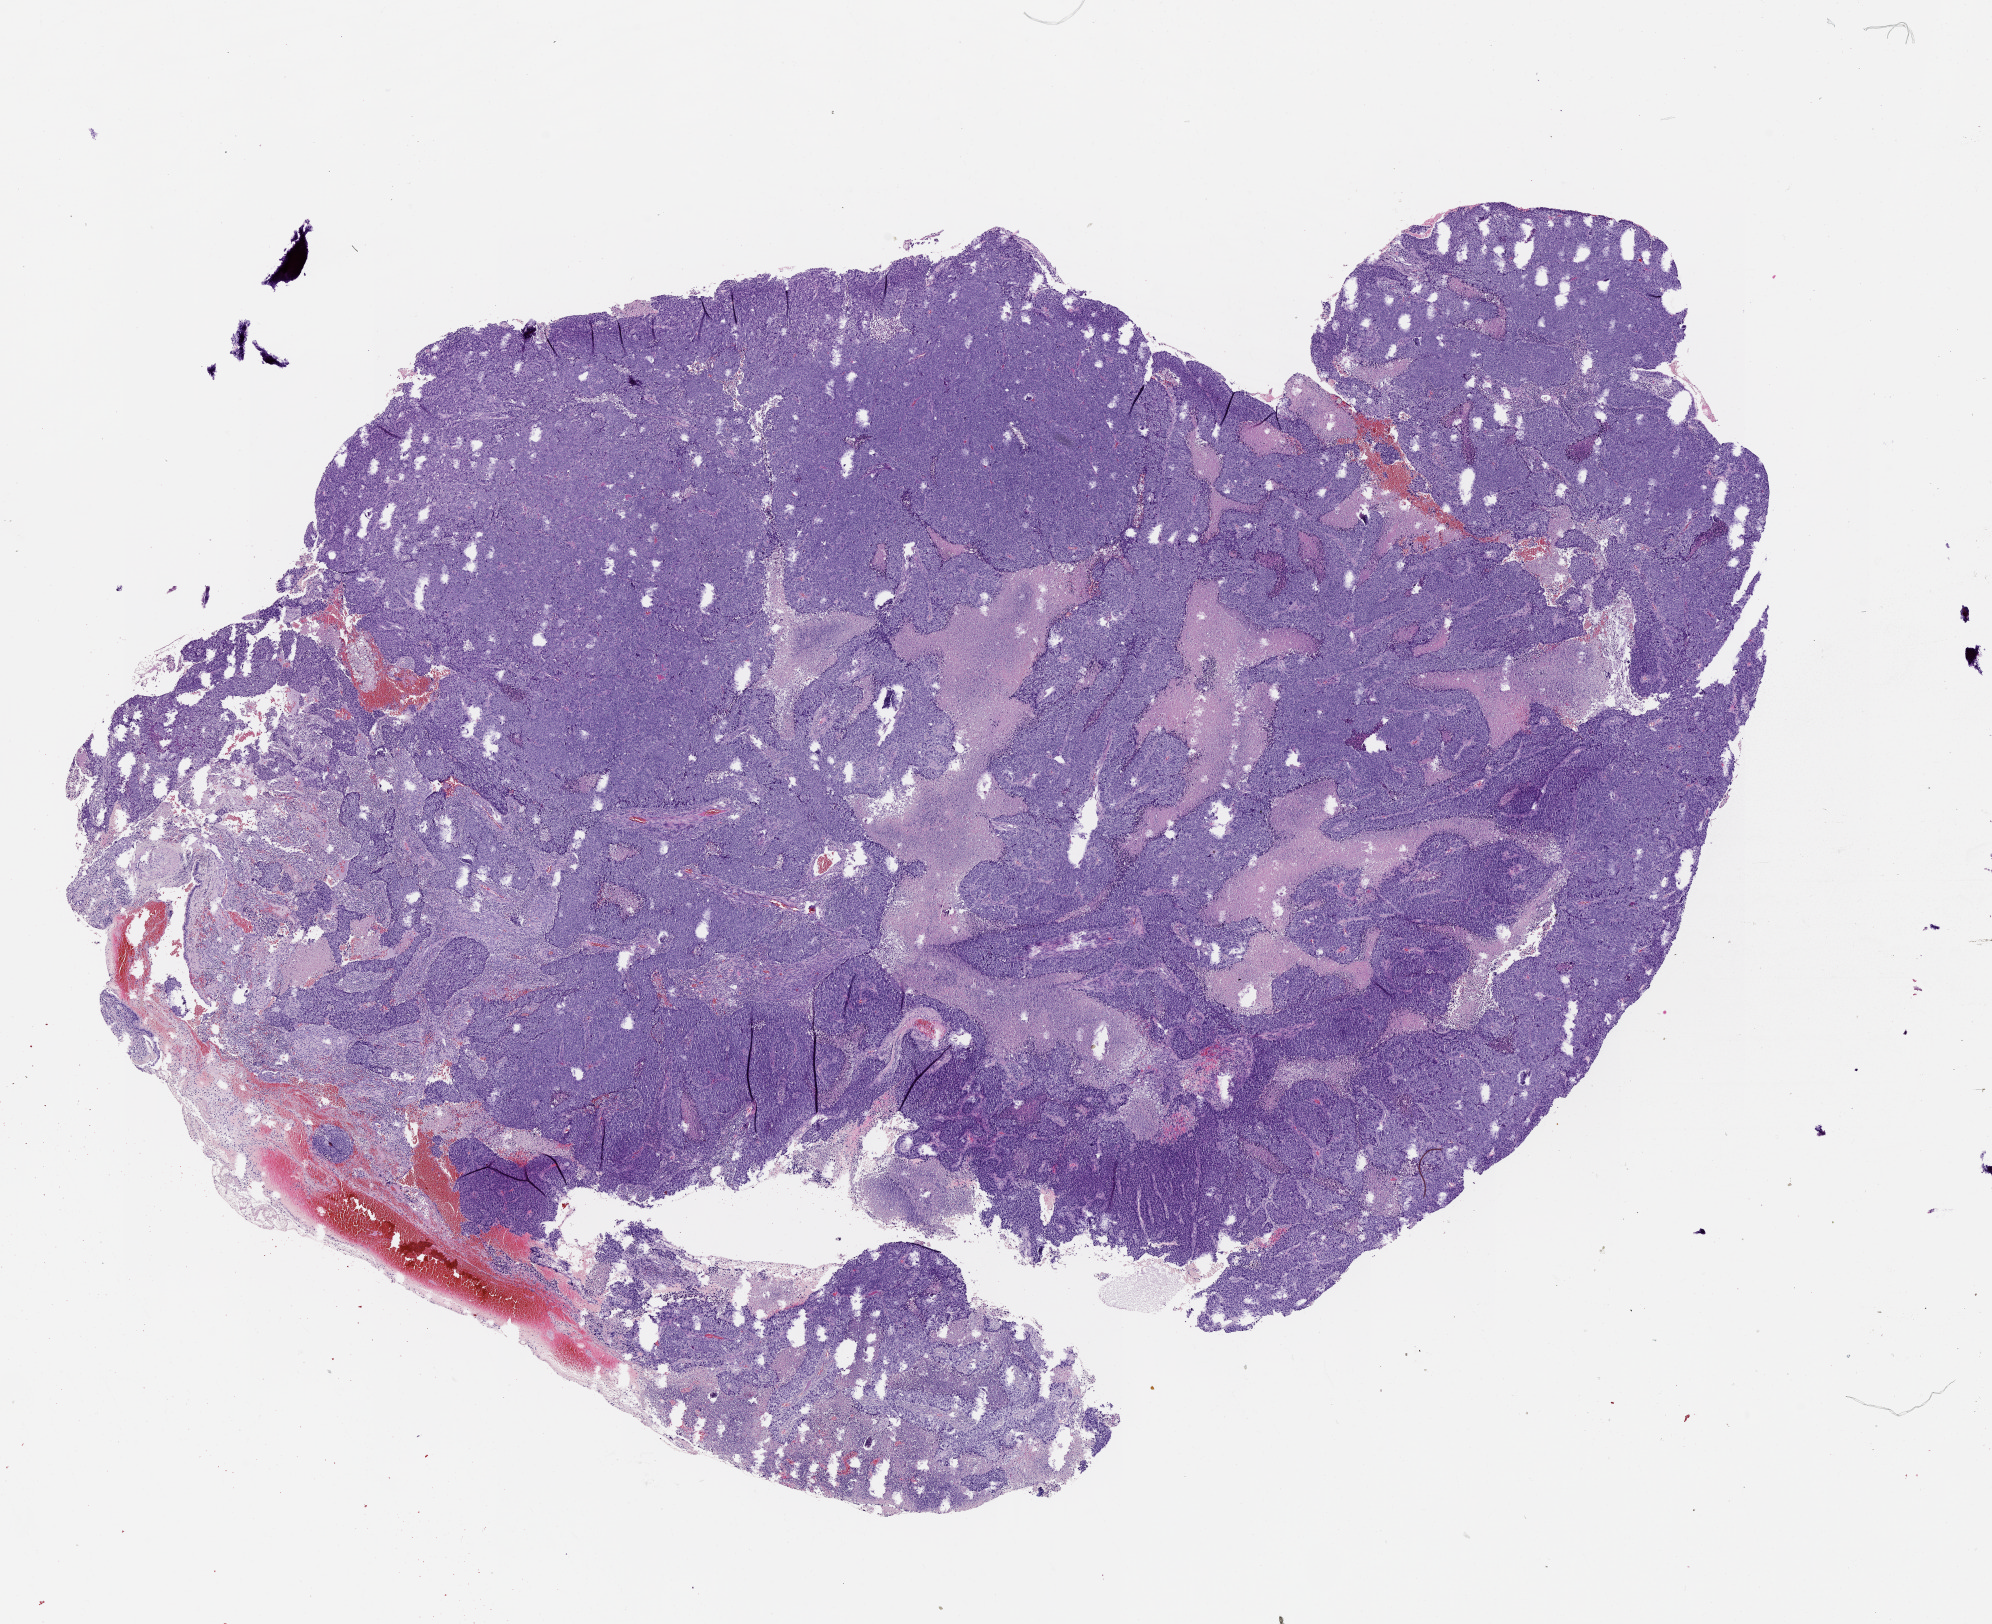
Digitized Hematoxylin and eosin (H&E) stained tissue section (whole slide) — whole scanned area (about 16.0 x 13.1 mm, acquisition: 20x scan) shown as a low-resolution overview. Tumour tissue sample, lung. Patient: male, age 60 years.
Patient diagnosis (cohort enrolment): squamous cell carcinoma (lung).